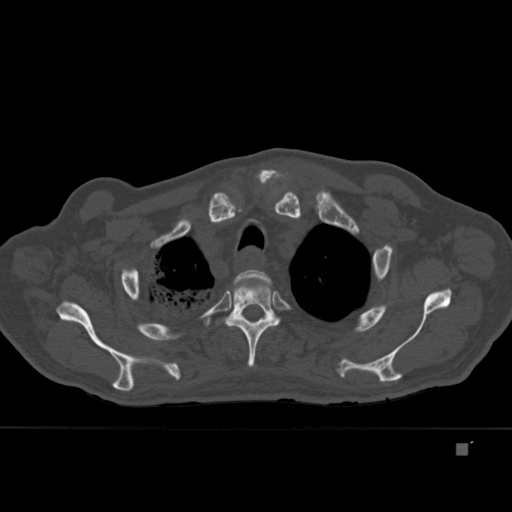
CT including the spine, one axial slice; position 335 of 451 along the scan axis; bone window (W 1800 / L 400 HU); 1.5 mm slice thickness; 512 × 512 image matrix, field of view 378 × 378 mm. Male patient, age 75 years. Case-level facts recorded for this patient, not image findings: primary cancer: prostate.
Outlined on this slice (semi-automatic segmentation, software-assisted and operator-edited):
- T2 vertebra: bounding box (x1, y1, x2, y2) in pixels: (224, 270, 275, 294)
- T3 vertebra: (222, 279, 281, 367)